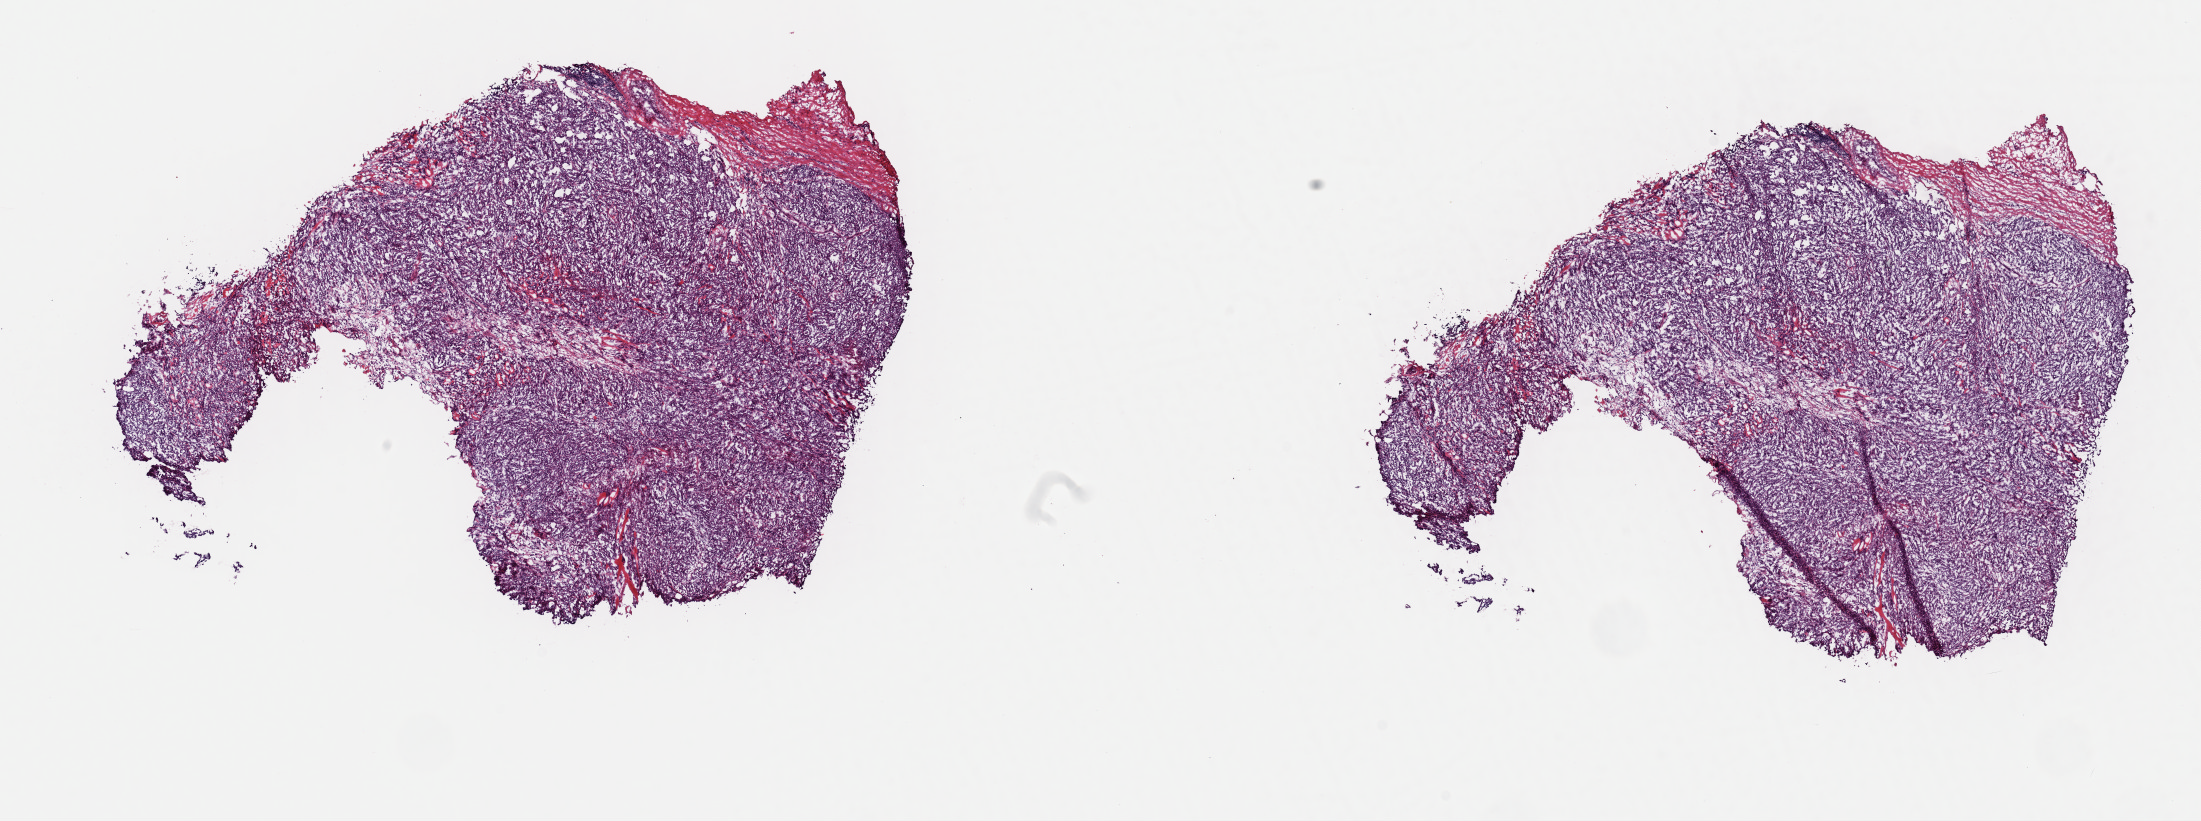
Hematoxylin and eosin (H&E) stained whole-slide image — whole scanned area (about 17.4 x 6.5 mm) shown as a low-resolution overview, frozen section, metastatic tumour sample, sampled site not recorded. Female, age 70 years at initial diagnosis. Pathologist review of this section (percent, as recorded): tumour cells 85%, tumour nuclei 85%, normal cells 0%, stromal cells 15%, necrosis 0%. Infiltration values recorded for this section: lymphocyte infiltration 3%, monocyte infiltration 0%, neutrophil infiltration 0%.
This section: metastatic tumour tissue. Patient diagnosis: Malignant melanoma, NOS.